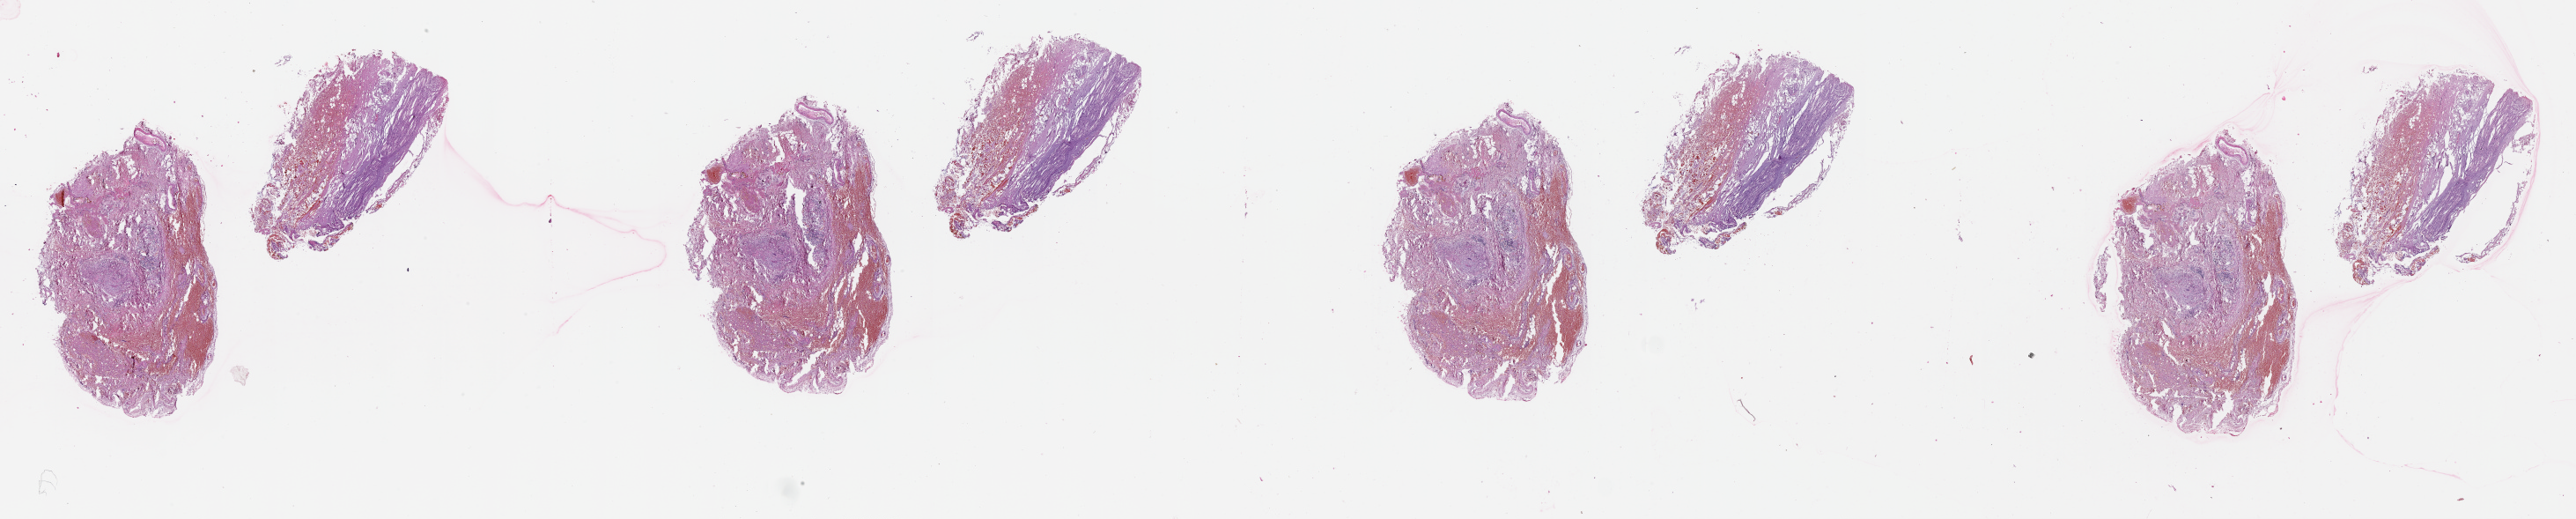
Whole-slide histology image, Hematoxylin and eosin (H&E) stained — shown as a low-resolution overview of the whole scanned area (about 47.1 x 9.5 mm). Lung, normal (non-tumour) tissue. Male, 72 y/o.
This section: normal (non-tumour) tissue from the same patient. Patient diagnosis (cohort enrolment): squamous cell carcinoma (lung).